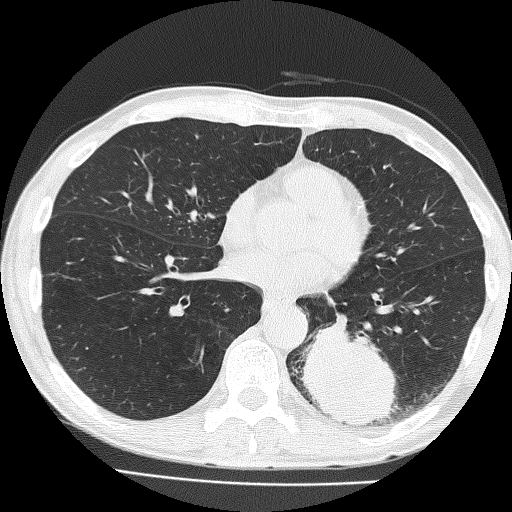
Low-dose screening chest CT, one axial slice; slice 71 of 160 in the series (ordered by position); reconstruction kernel FC51; 120 kVp; lung window (W 1500 / L -600 HU); 2 mm slice thickness; 512 × 512 image matrix, field of view 324 × 324 mm.
Structures marked on this image (expert manual segmentation):
- lesion 1 (tumor, lower lobe of left lung): bounding box [x1, y1, x2, y2] px = [301, 319, 398, 426]